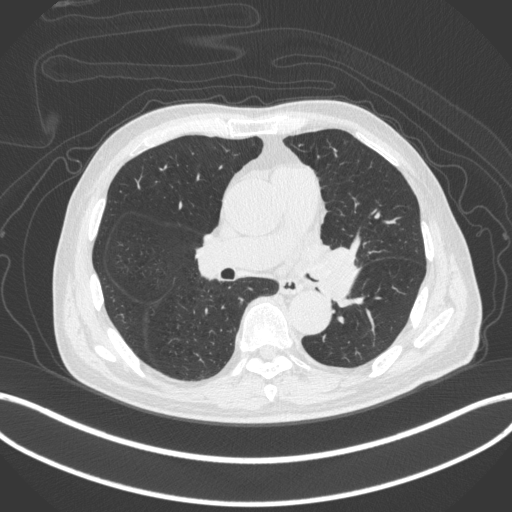
Chest CT, one axial slice; position 235 of 420 along the scan axis; reconstruction kernel B31f; 120 kVp; lung window (W 1500 / L -600 HU); 512 × 512 image matrix. Male patient, age 77 years. Case-level facts recorded for this patient, not image findings: clinical TNM (as recorded): T3 N1 M0.
Structures marked on this image (rectangle marked by the reading radiologist):
- lung tumour (recorded histology: adenocarcinoma): bounding box <311,236,365,305> (left, top, right, bottom; pixels)